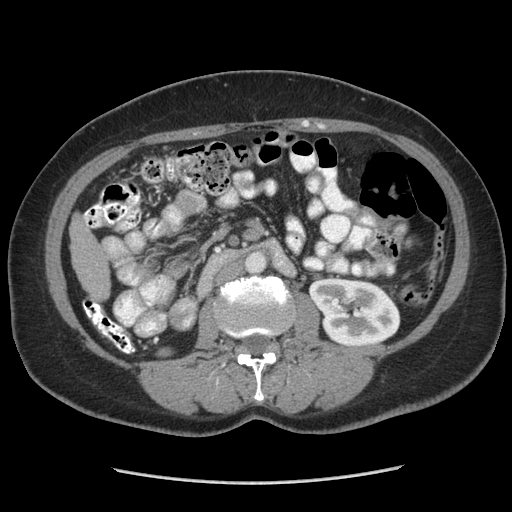
Contrast-enhanced abdominal CT (liver protocol), one axial slice; slice 114 of 185 in the series (ordered by position); reconstruction kernel STANDARD; soft-tissue window (W 400 / L 40 HU); 2.5 mm slice thickness; 512 × 512 image matrix. Case-level facts recorded for this patient, not image findings: diagnosis: hepatocellular carcinoma (patient treated with transarterial chemoembolisation; whether this scan precedes or follows treatment is not stated here); TNM stage (as recorded): Stage-I; Child-Pugh class: A; tumour differentiation: poorly differentiated; tumour nodularity: uninodular.
Annotated regions visible in this slice (semi-automatically segmented with operator editing):
- liver parenchyma outside the tumour (the mass and vessels are separate outlines, so this box may not span the whole liver): box from (x=70, y=214) to (x=110, y=300) px